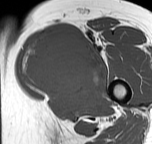
MRI of an extremity soft-tissue mass, one axial slice; slice 37 of 57 in the series (ordered by position); MR volume resampled by the dataset authors to the PET/CT grid (not the native acquisition matrix); 3.27 mm slice thickness; 152 × 144 image matrix. Female patient. Case-level facts recorded for this patient, not image findings: histological type: pleiomorphic leiomyosarcoma; grade: intermediate; site of the primary tumour: left thigh.
Annotated regions visible in this slice (expert contour drawn on MRI and transferred to this co-registered scan by the dataset authors):
- gross tumour volume including surrounding oedema: box from (x=20, y=33) to (x=103, y=100) px
- gross tumour volume (mass): (x=20, y=33)–(x=103, y=100)